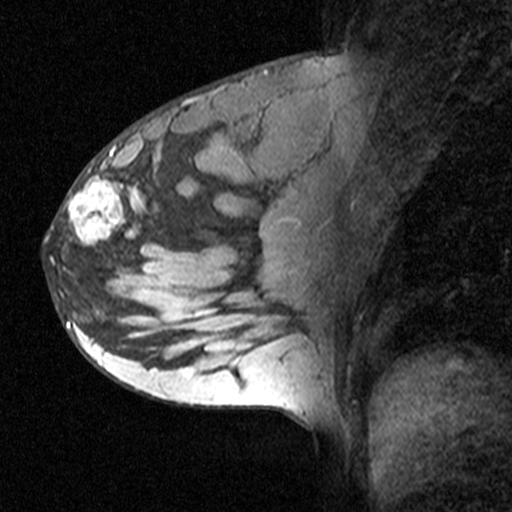
Breast MRI (dynamic contrast-enhanced), one sagittal slice; position 22 of 44 along the scan axis; dynamic contrast-enhanced study with each time point stored as its own series, time point 2 of 3 at this slice position (early post-contrast, ordered by acquisition time); 1.5 T; TE 4.5 ms, TR 11 ms; 3 mm slice thickness; 512 × 512 image matrix, field of view 200 × 200 mm. Female patient, age 27 years. From the clinical record (not read from this slice): setting: breast cancer imaged before/during neoadjuvant chemotherapy; receptor status: HR-positive, HER2-negative.
Annotated regions visible in this slice (semi-automatically segmented with operator editing):
- analysis volume of interest (the breast-tissue region the enhancement analysis was run in; not a lesion): bounding box <44,162,163,271> (left, top, right, bottom; pixels)
- tumour enhancement mask (voxels above the 90 % enhancement threshold inside the analysis volume of interest): <67,162,143,254>